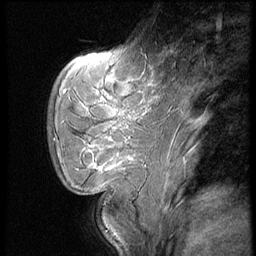
Breast MRI (dynamic contrast-enhanced), one sagittal slice; position 16 of 62 along the scan axis; dynamic contrast-enhanced series, image 2 of 4 at this slice position (ordered by acquisition); 1.5 T; TE 4.2 ms, TR 9 ms; 256 × 256 image matrix, field of view 180 × 180 mm. Patient: female, 28 years. From the clinical record (not read from this slice): setting: breast cancer imaged before/during neoadjuvant chemotherapy.
Structures marked on this image (semi-automatic segmentation, software-assisted and operator-edited):
- analysis volume of interest (the breast-tissue region the enhancement analysis was run in; not a lesion): bounding box (x1, y1, x2, y2) in pixels: (50, 54, 150, 183)
- tumour enhancement mask (voxels above the 140 % enhancement threshold inside the analysis volume of interest): (96, 165, 118, 169)